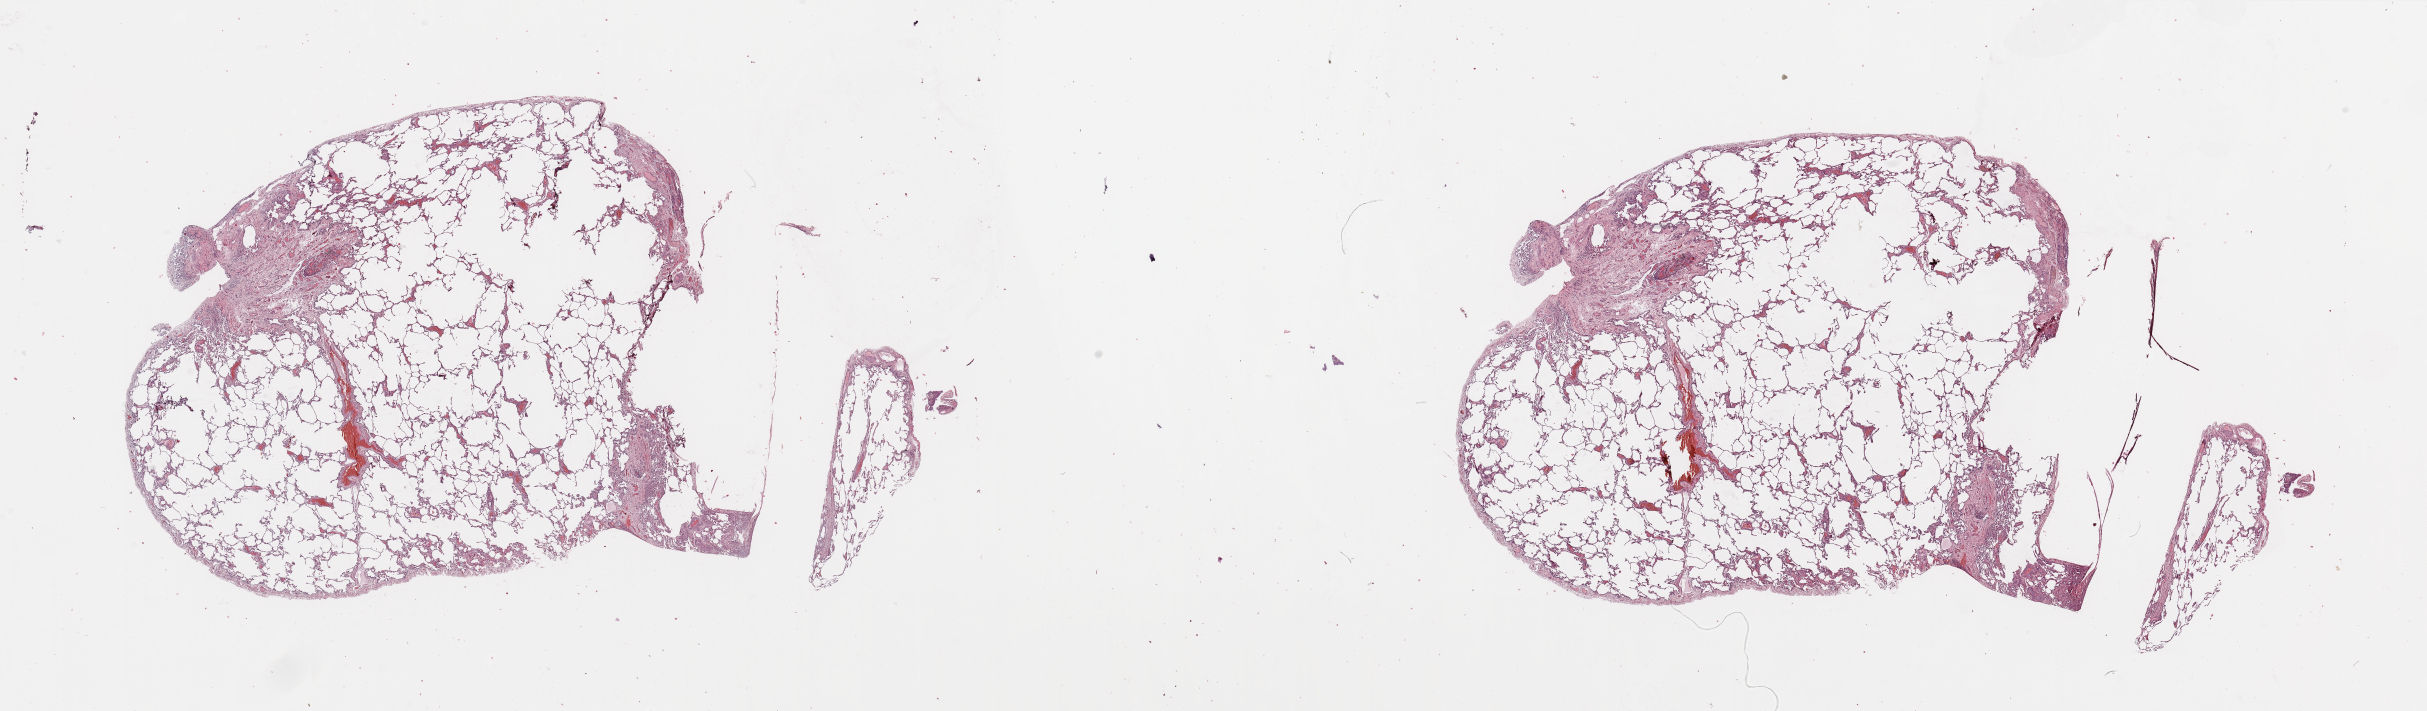
Whole-slide histology image, Hematoxylin and eosin (H&E) stained — whole scanned area (about 38.4 x 11.2 mm) shown as a low-resolution overview; normal (non-tumour) tissue sample, sampled site: lung. Male, 57 y/o.
- this section: normal (non-tumour) tissue from the same patient
- patient diagnosis: Squamous cell carcinoma, NOS